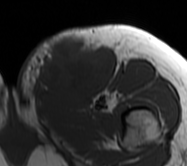
MRI of an extremity soft-tissue mass, one axial slice. Position 22 of 62 along the scan axis. MR volume resampled by the dataset authors to the PET/CT grid (not the native acquisition matrix). 3.27 mm slice thickness. 187 × 166 image matrix. Female patient. Case-level facts recorded for this patient, not image findings: histological type: leiomyosarcoma; grade: high; site of the primary tumour: groin.
Structures marked on this image (expert contour drawn on MRI and transferred to this co-registered scan by the dataset authors):
- gross tumour volume including surrounding oedema: bounding box <16,26,115,109> (left, top, right, bottom; pixels)
- gross tumour volume (mass): <39,37,115,104>